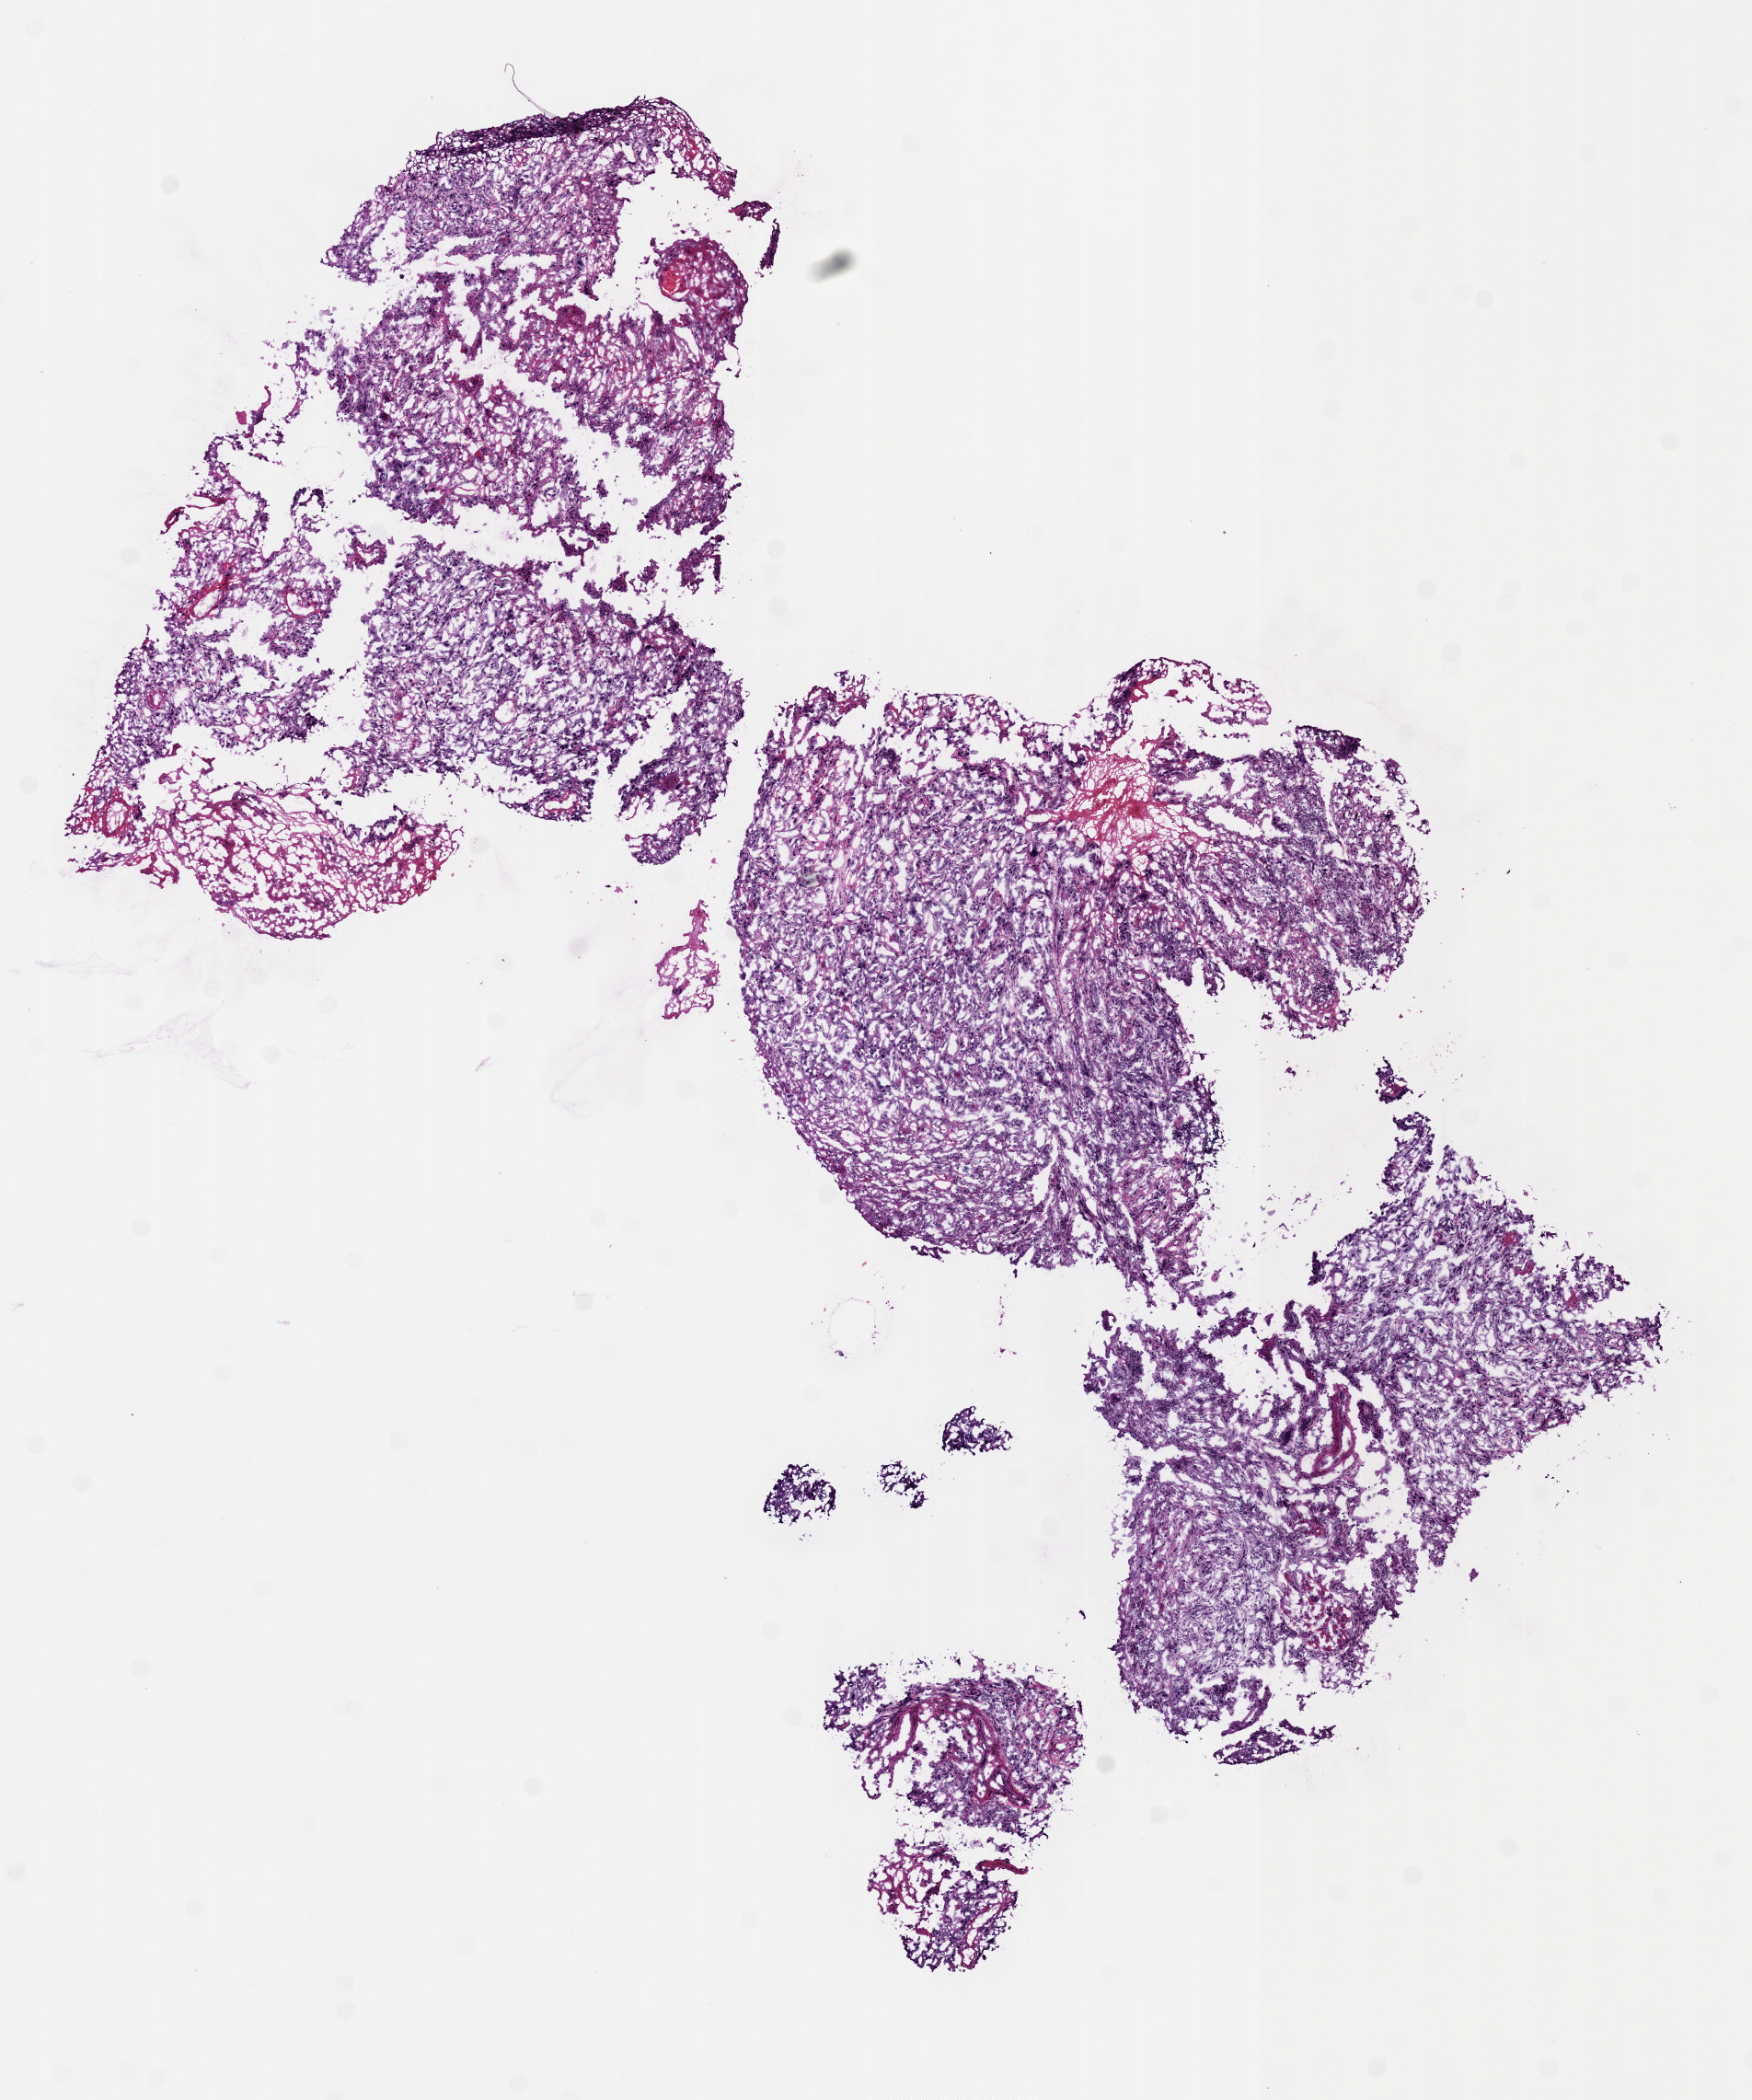
Hematoxylin and eosin (H&E) stained whole-slide image — whole scanned area (about 7.5 x 9.0 mm, acquisition: 40x scan) shown as a low-resolution overview. Frozen section from the top of the tissue portion. Head and neck, primary tumour sample. Male patient; age at initial diagnosis 41 years. Histologic grade: G3 (poorly differentiated). Slide review estimates, as recorded: tumour cells 50%, tumour nuclei 60%, normal cells 0%, stromal cells 50%, necrosis 0%. Infiltration values recorded for this section: lymphocyte infiltration 10%, monocyte infiltration 0%, neutrophil infiltration 0%.
Pathologic diagnosis: Squamous cell carcinoma, NOS (tongue, NOS). TNM: T1 NX MX. AJCC pathologic stage: I (6th edition). Laterality: right.